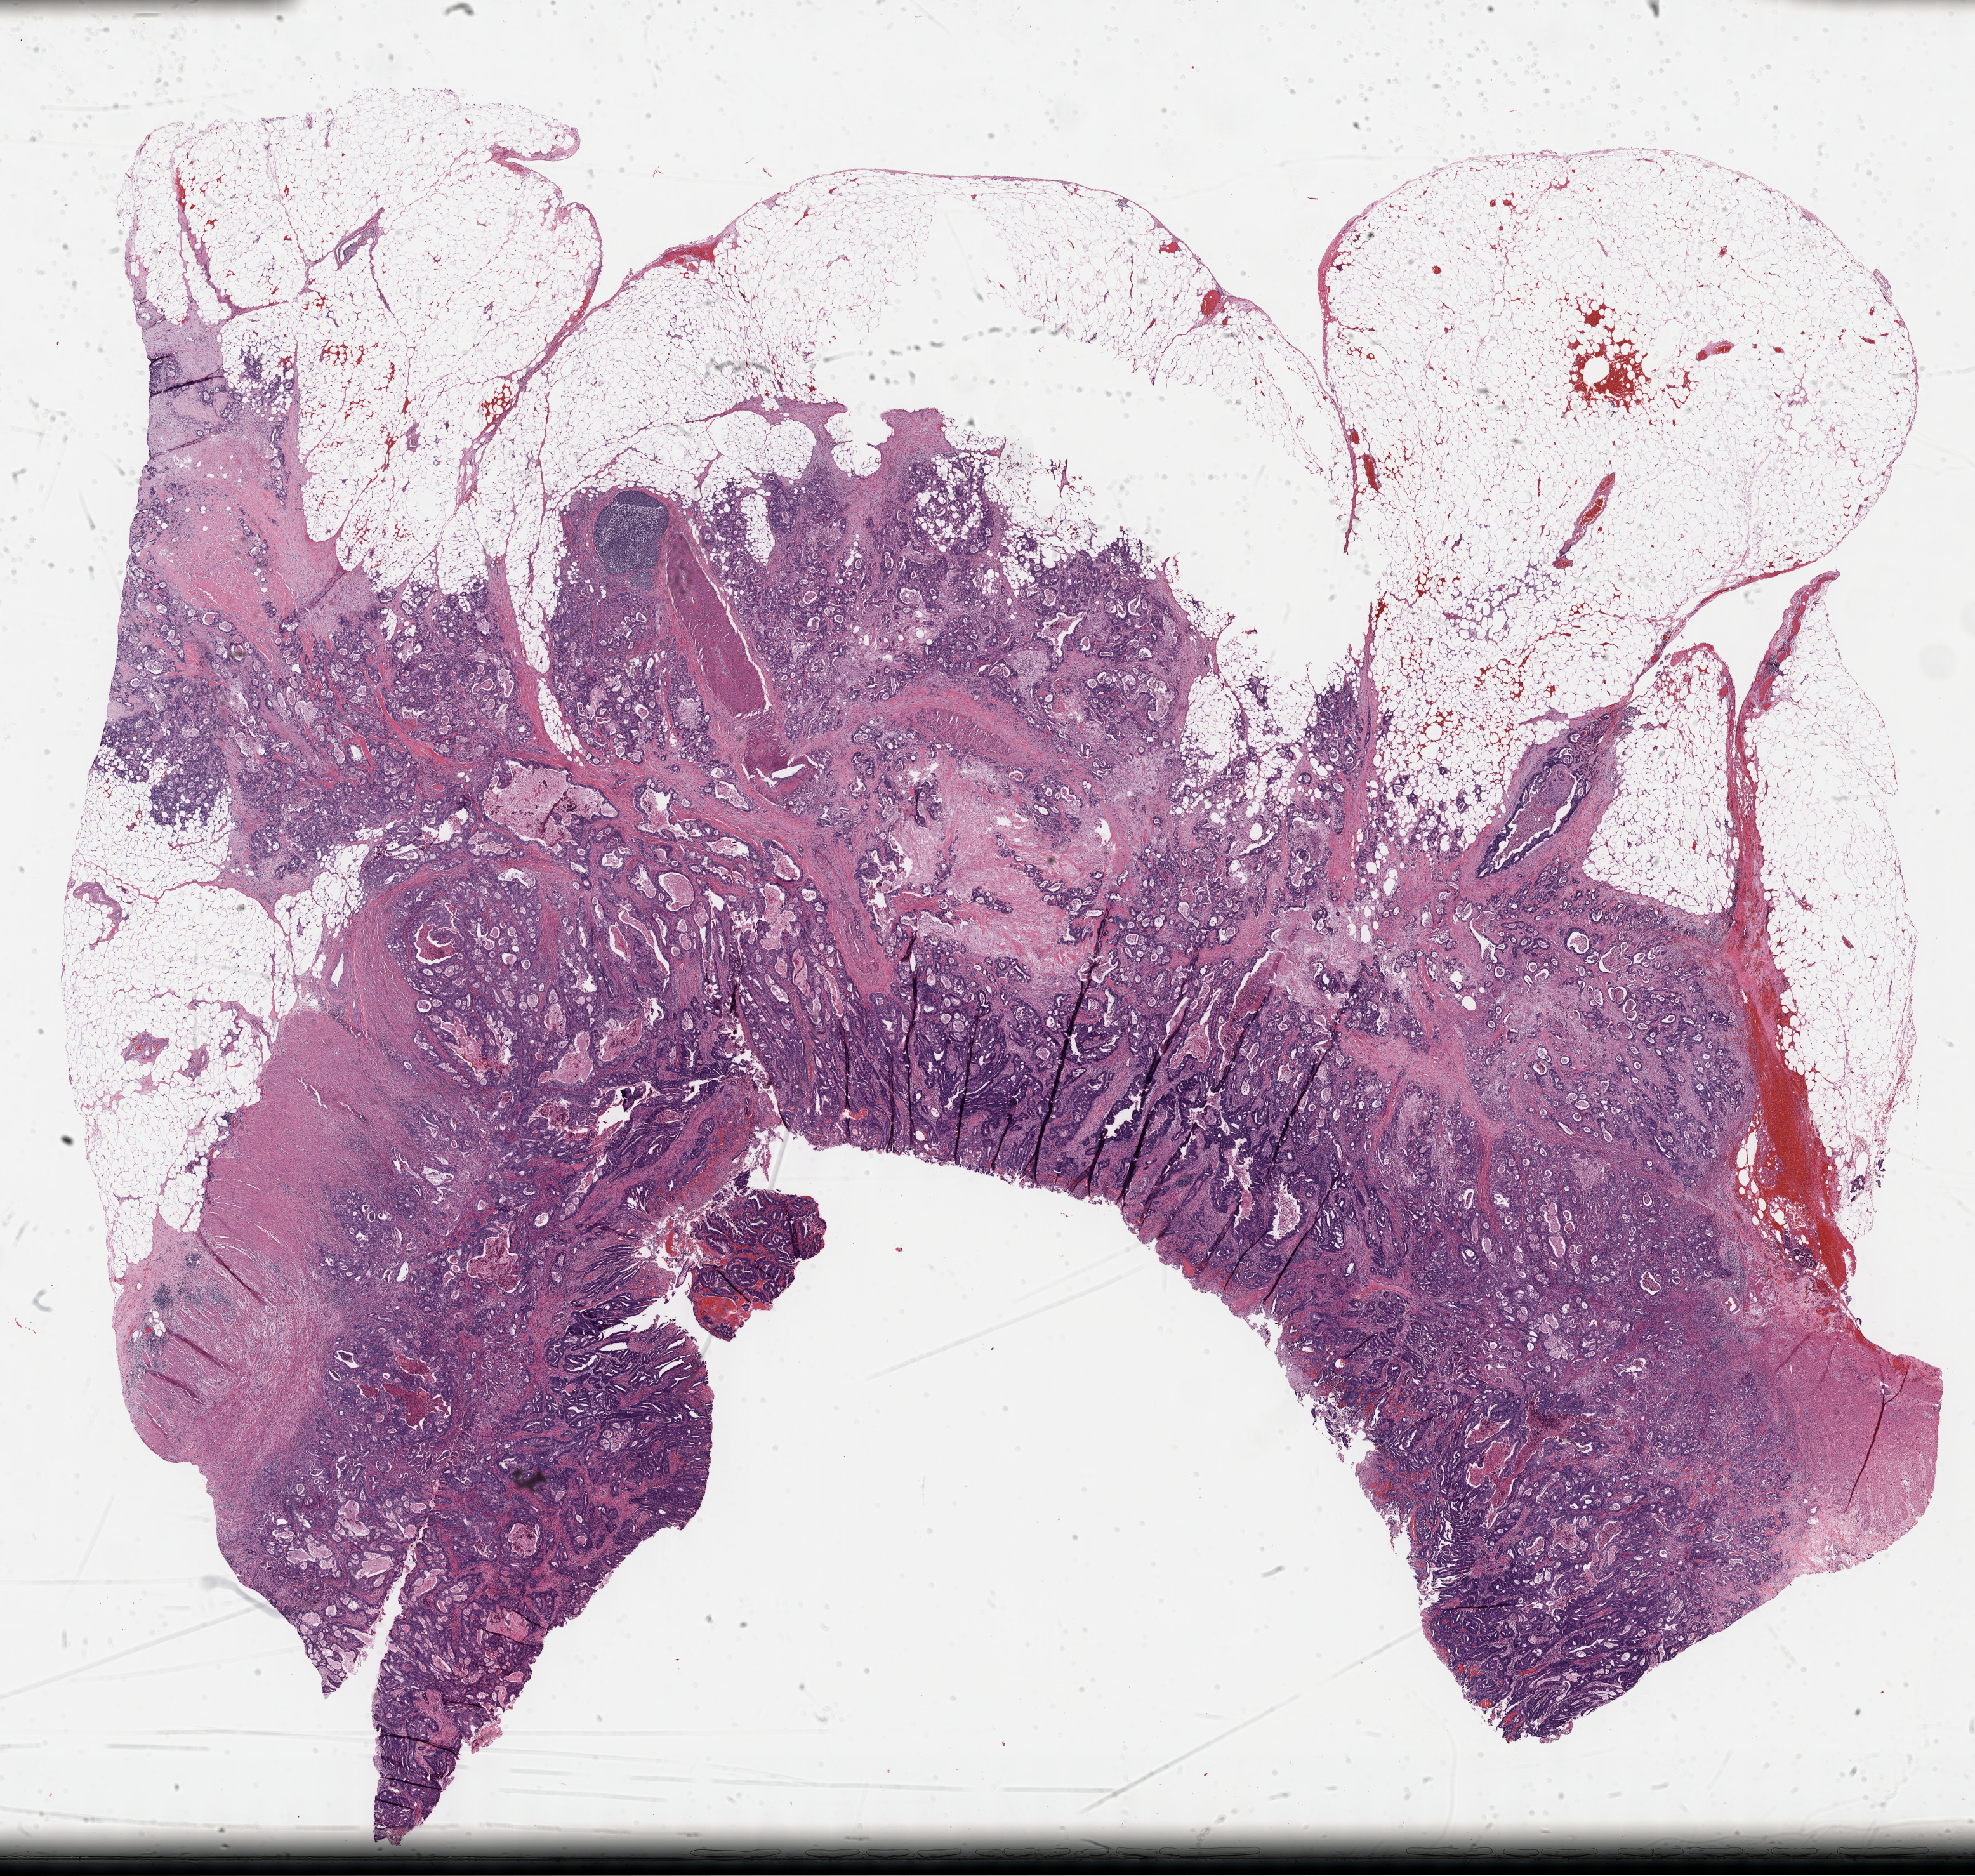
Whole-slide histology image, H&E — low-resolution overview of the scanned area, about 25.2 x 23.9 mm (slide scanned at 40x), formalin-fixed paraffin-embedded (FFPE) diagnostic section, colon, primary tumour sample. Patient: male, age at initial diagnosis 67 years.
Diagnosis: Adenocarcinoma, NOS (ascending colon). AJCC pathologic stage: IIIB.